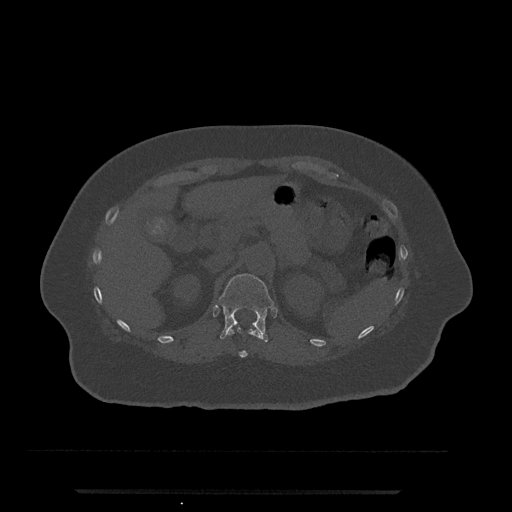
CT including the spine, one axial slice. Slice 188 of 797 in the series (ordered by position). Reconstruction kernel Br40s/3. 120 kVp. Bone window (W 1800 / L 400 HU). 0.5 mm slice thickness. 512 × 512 image matrix, field of view 440 × 440 mm. Patient: female, 51 years. From the clinical record (not read from this slice): primary cancer: neuro; vertebrae with lytic lesions (as recorded): T8.
Outlined on this slice (semi-automatic segmentation, software-assisted and operator-edited):
- T11 vertebra: bounding box (x1, y1, x2, y2) in pixels: (228, 326, 261, 358)
- T12 vertebra: (218, 274, 274, 342)